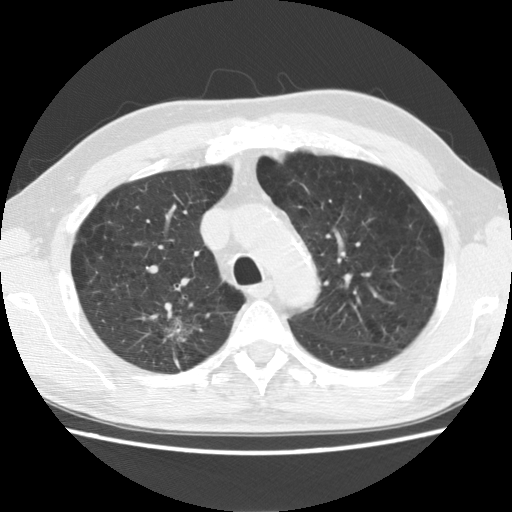
Chest CT (low-dose screening protocol), one axial image, baseline screening round, lung window (W 1500 / L -600 HU), 2.5 mm slice thickness, standard (soft-tissue) reconstruction kernel (STANDARD). Male, age 64 years at enrolment.
• Lesion marked by an expert reader, box from (x=118, y=297) to (x=210, y=368) px.
• Reader record for this screening exam (exam-level; its link to the box is not recorded): non-calcified nodule or mass ≥4 mm, right upper lobe, 39 × 31 mm, spiculated (stellate) margins, mixed attenuation.
• Participant outcome: lung cancer diagnosed 74 days after this screen — adenocarcinoma, NOS, right upper lobe, moderately differentiated (G2), stage IB (AJCC 6th edition), 40 mm at pathology.